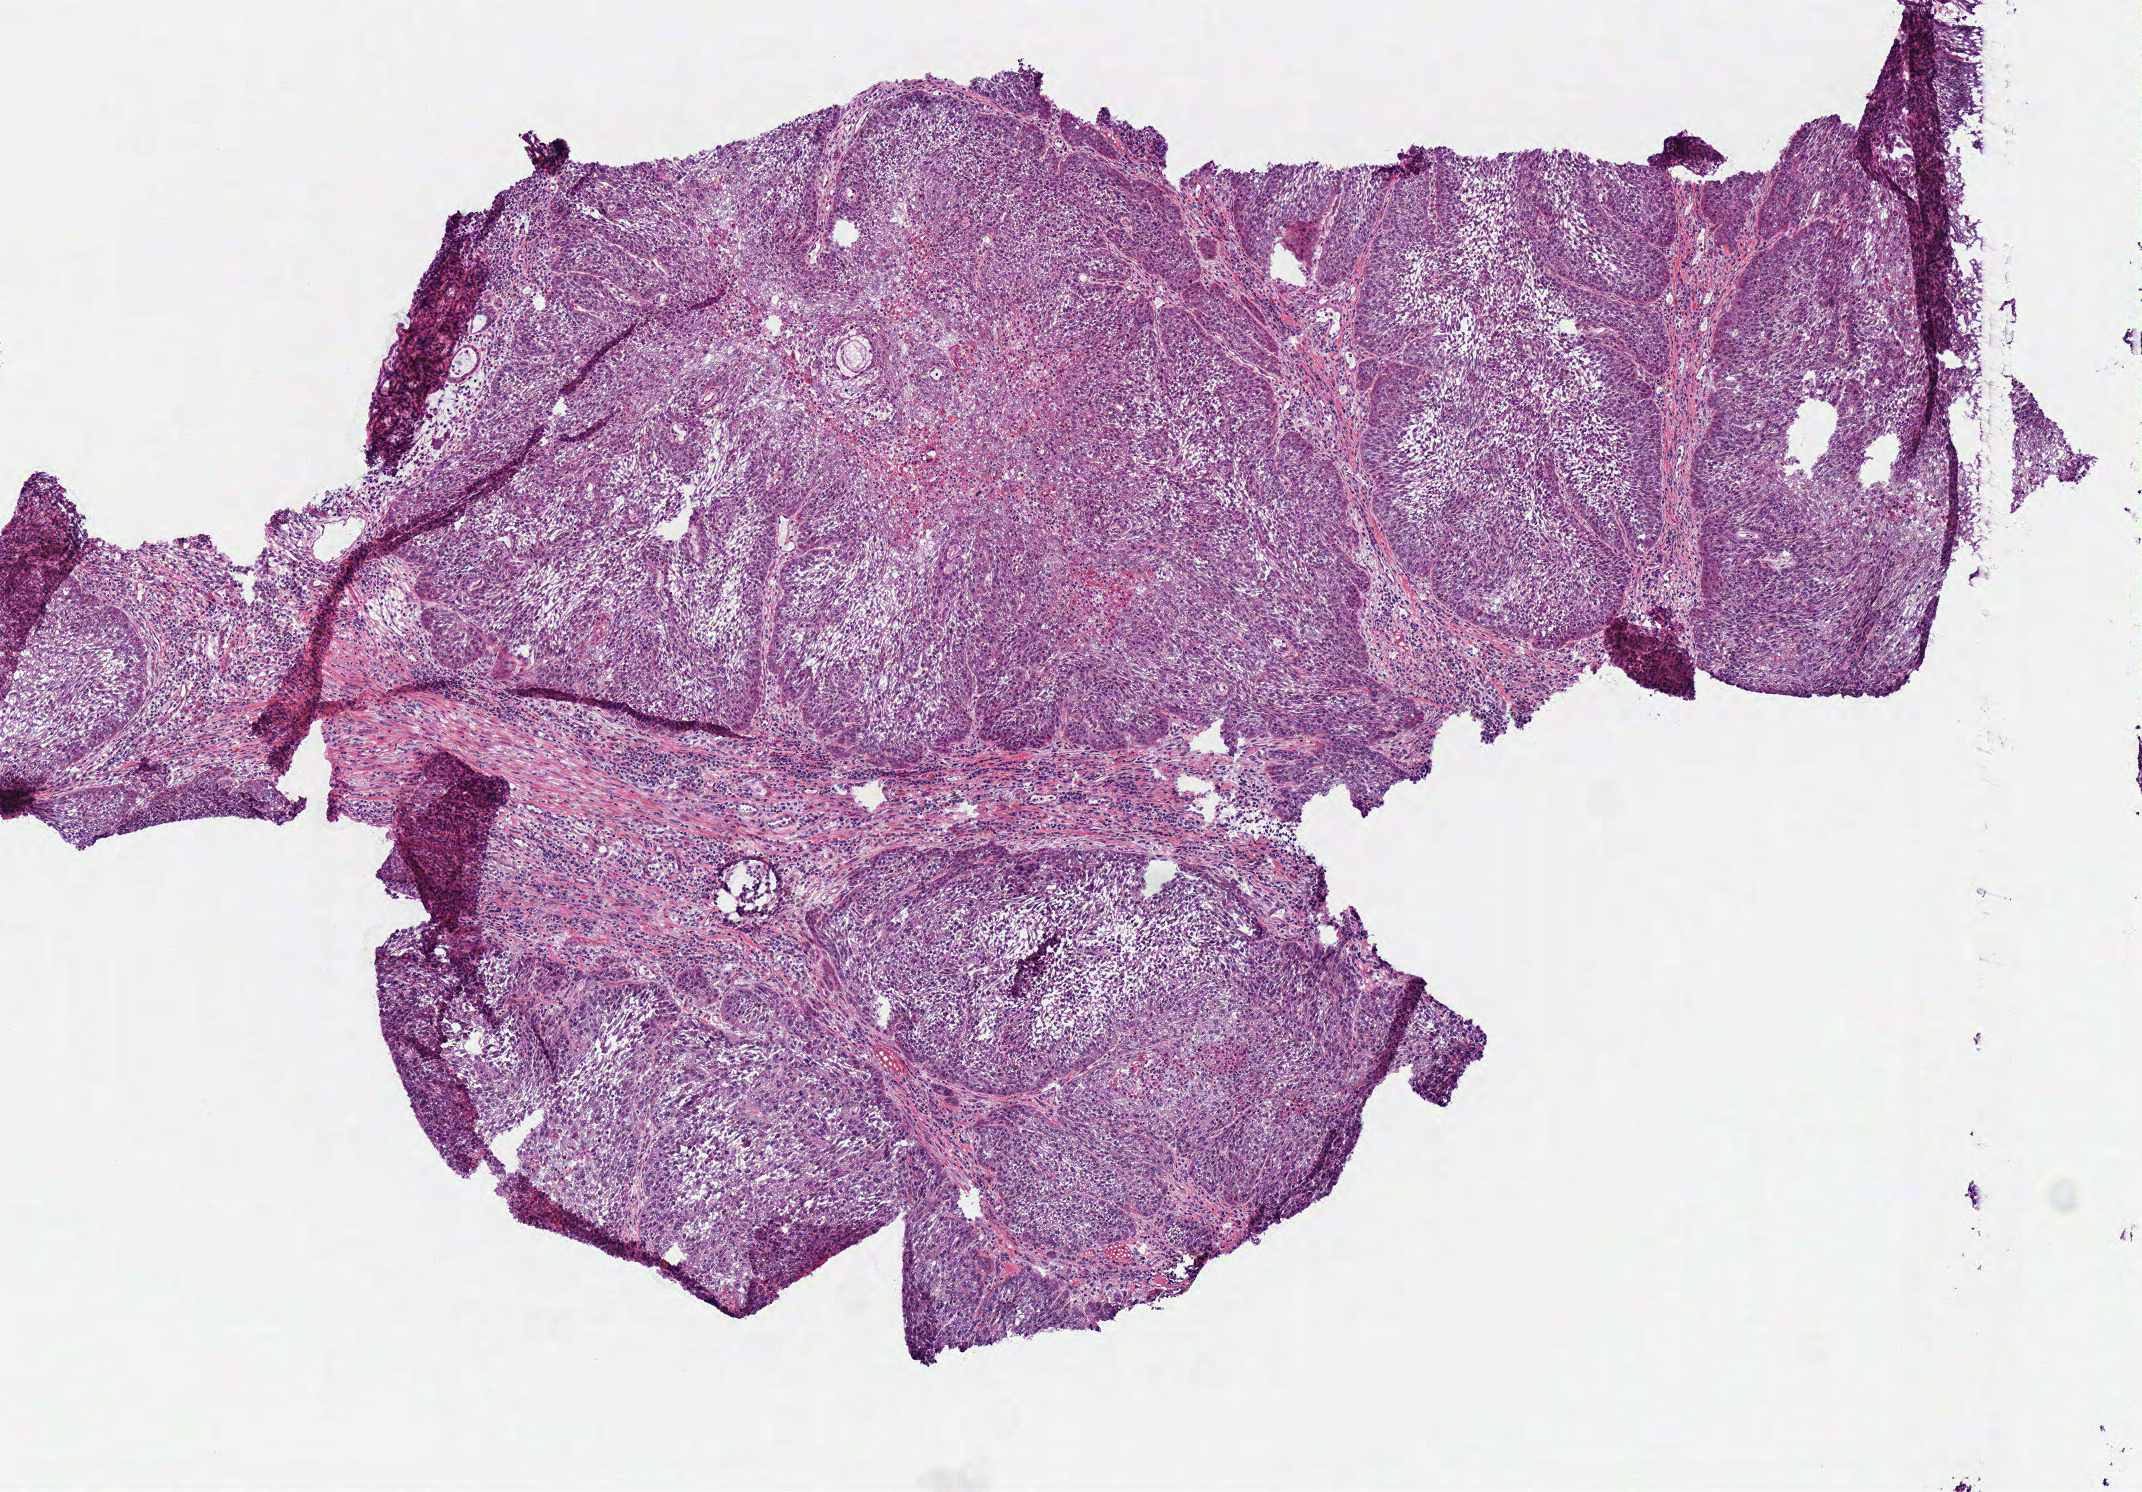
Hematoxylin and eosin (H&E) stained whole-slide image, a low-resolution overview of the entire scanned area, about 4.2 x 2.9 mm (from a 40x scan); frozen section; sample: primary tumour, head and neck. Patient: male, age at initial diagnosis 62 years.
Histologic diagnosis: Squamous cell carcinoma, NOS (larynx, NOS).